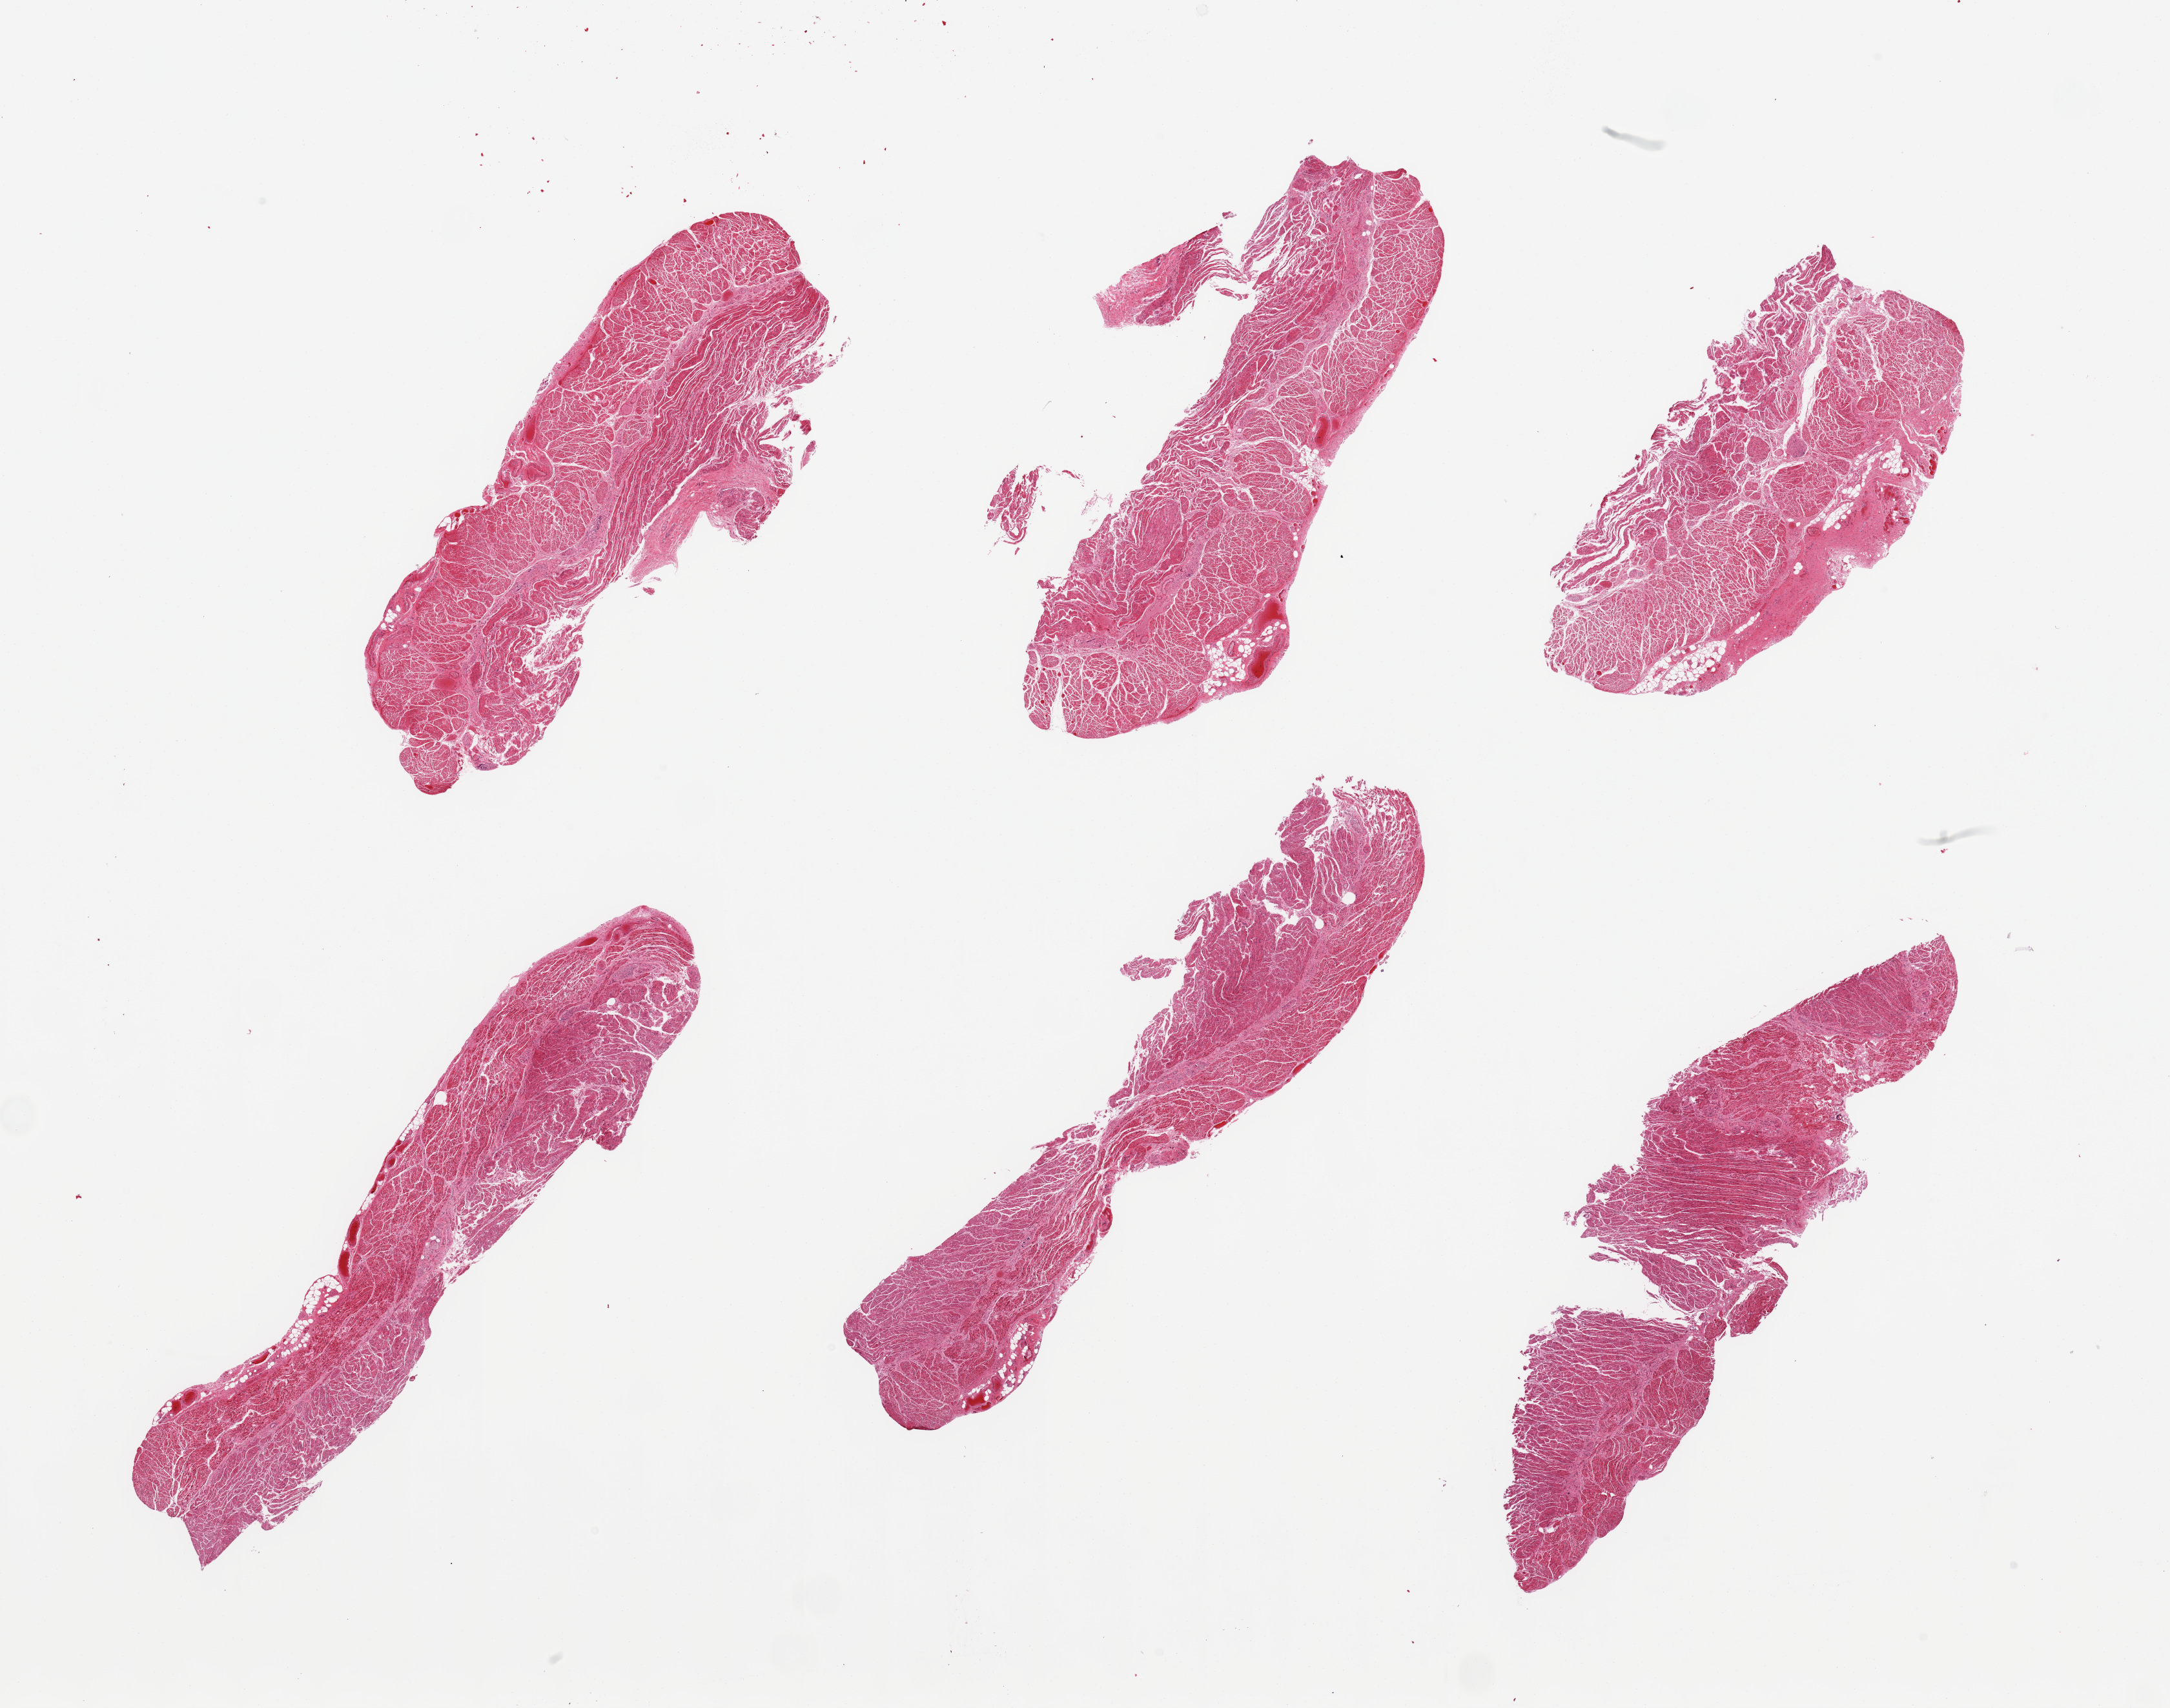
Whole-slide image, hematoxylin and eosin (H&E) stain, shown as a low-resolution overview of the whole scanned area (about 26.6 x 20.9 mm), PAXgene-fixed, paraffin-embedded tissue, sampled site (target tissue): gastroesophageal junction, donor tissue sample. Donor: male.
Pathologist's review note for this sample: 6 pieces, confirmed target muscularis.